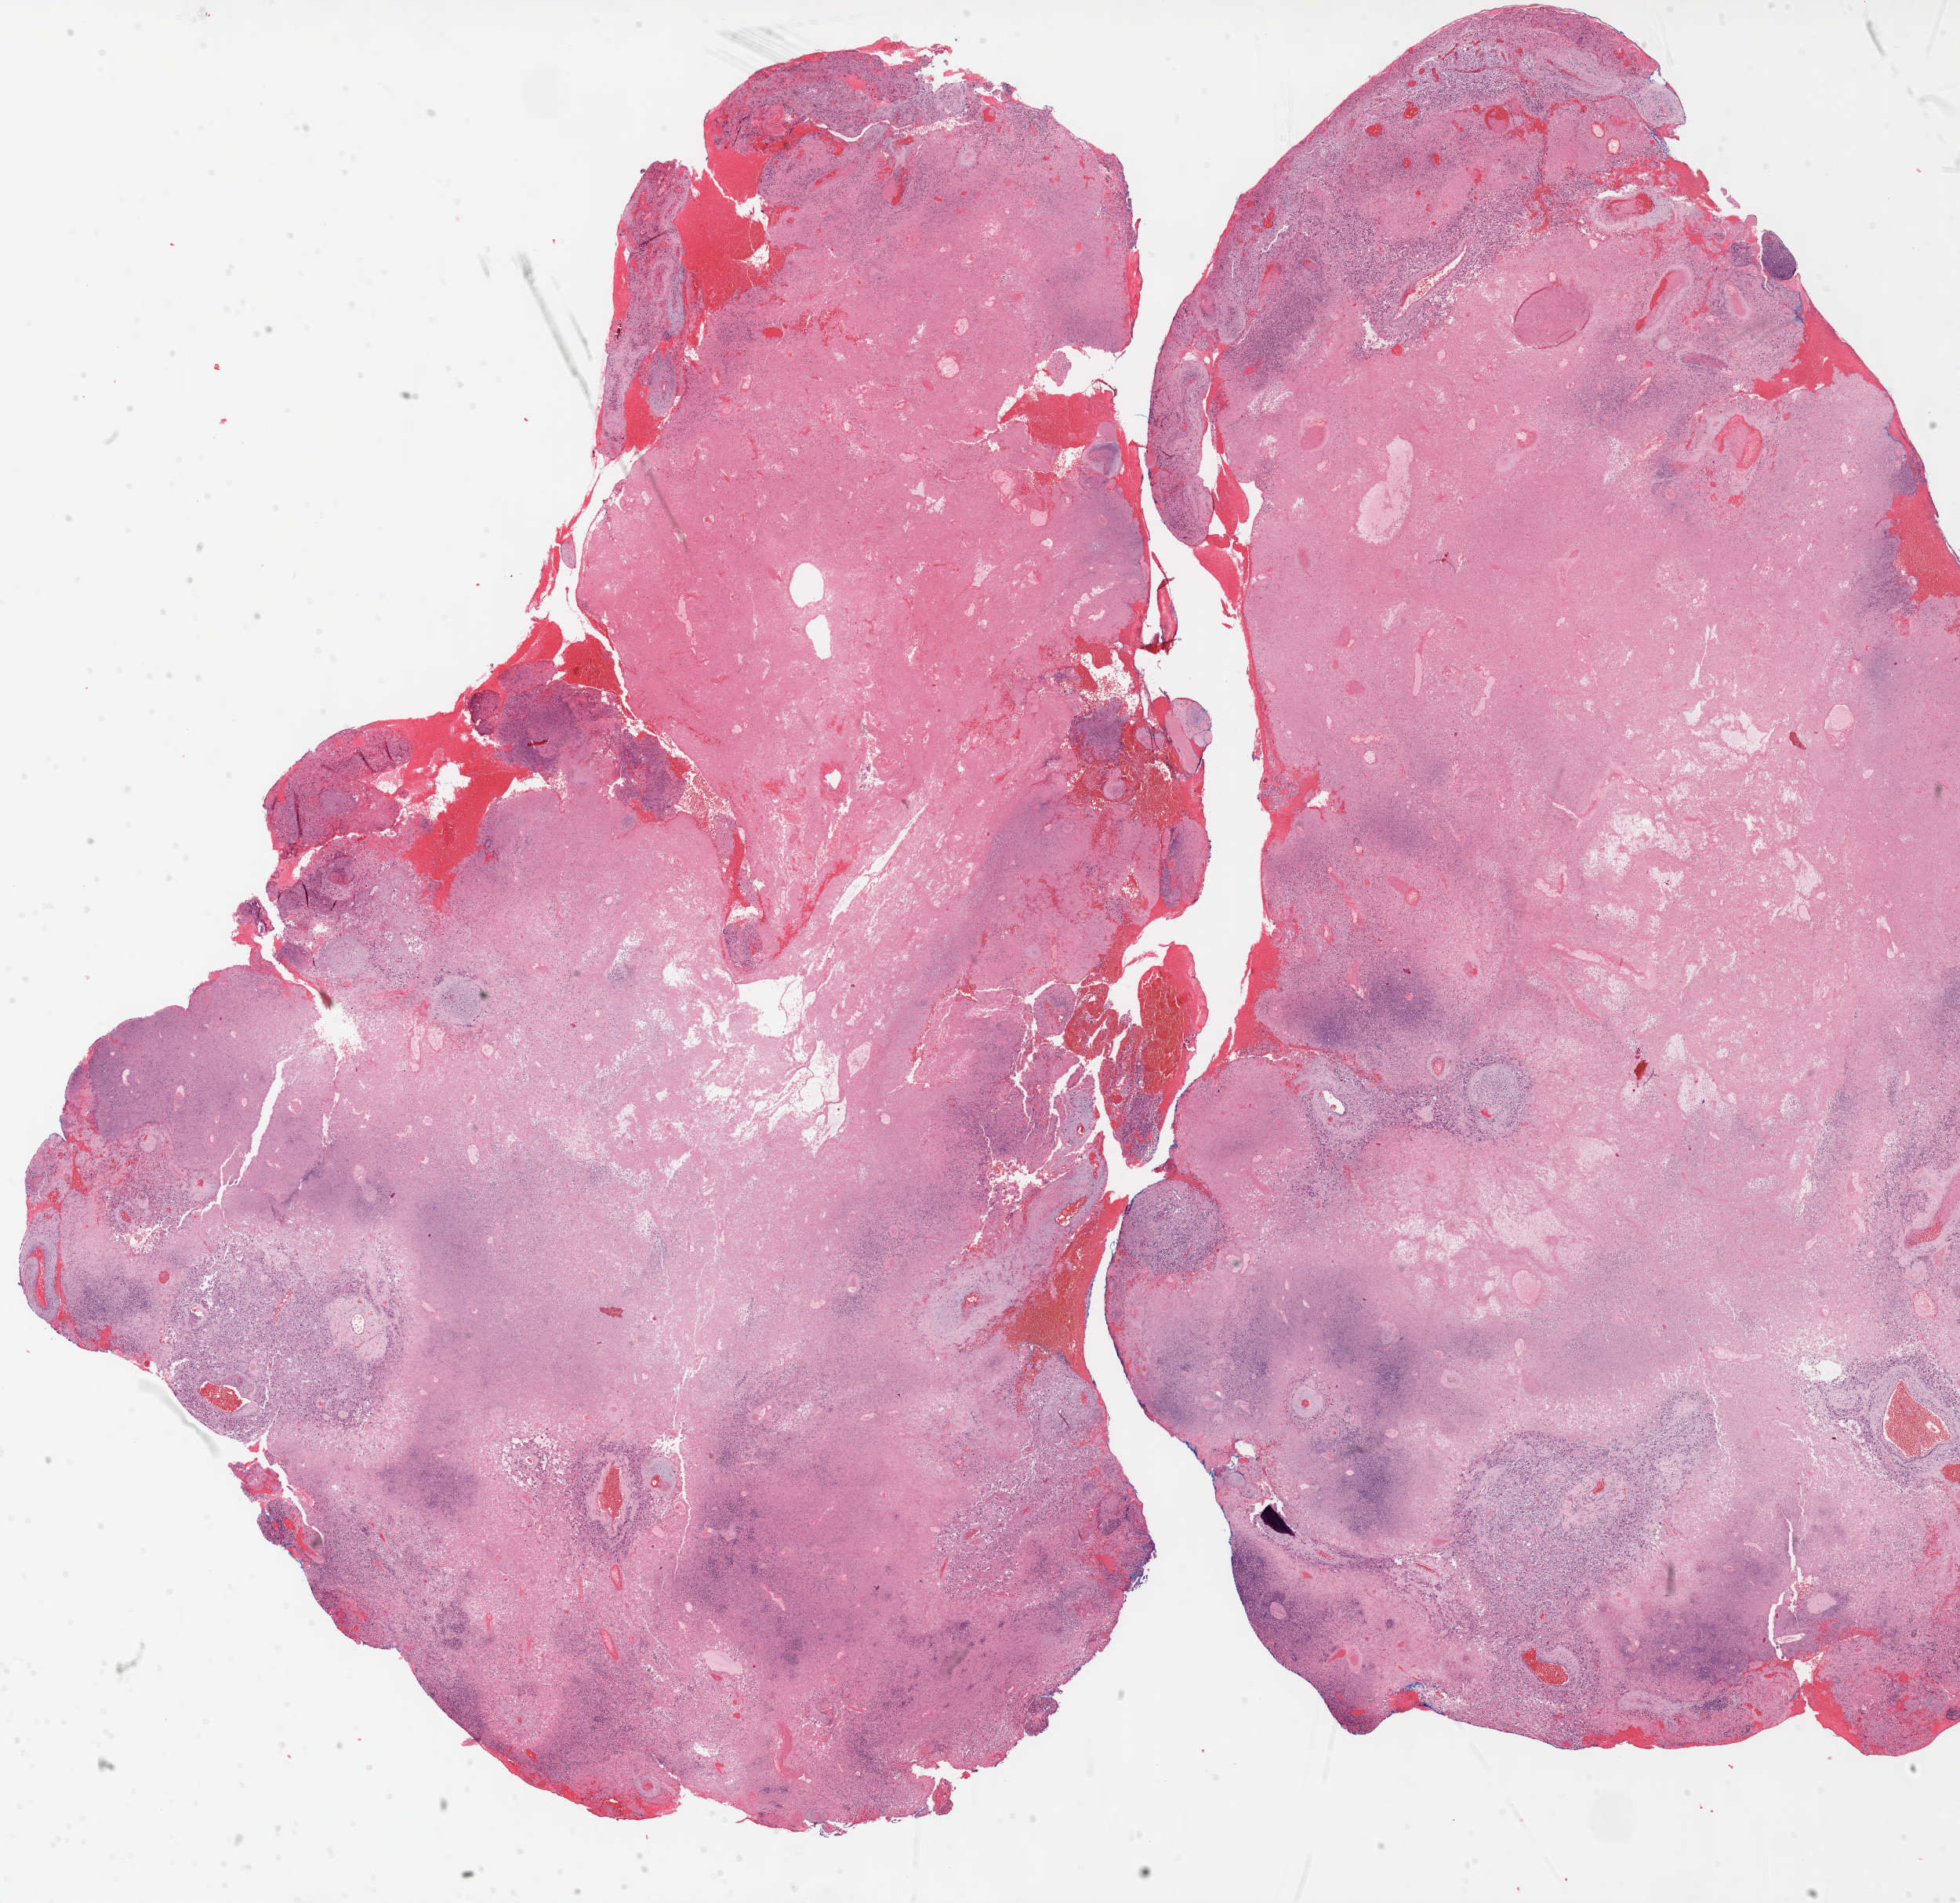
Digitized H&E tissue section (whole slide) — whole scanned area (about 20.1 x 19.5 mm, from a 20x scan) shown as a low-resolution overview. FFPE section. Primary tumour sample from the brain. Patient: male, age at initial diagnosis 66 years.
• diagnosis: Glioblastoma